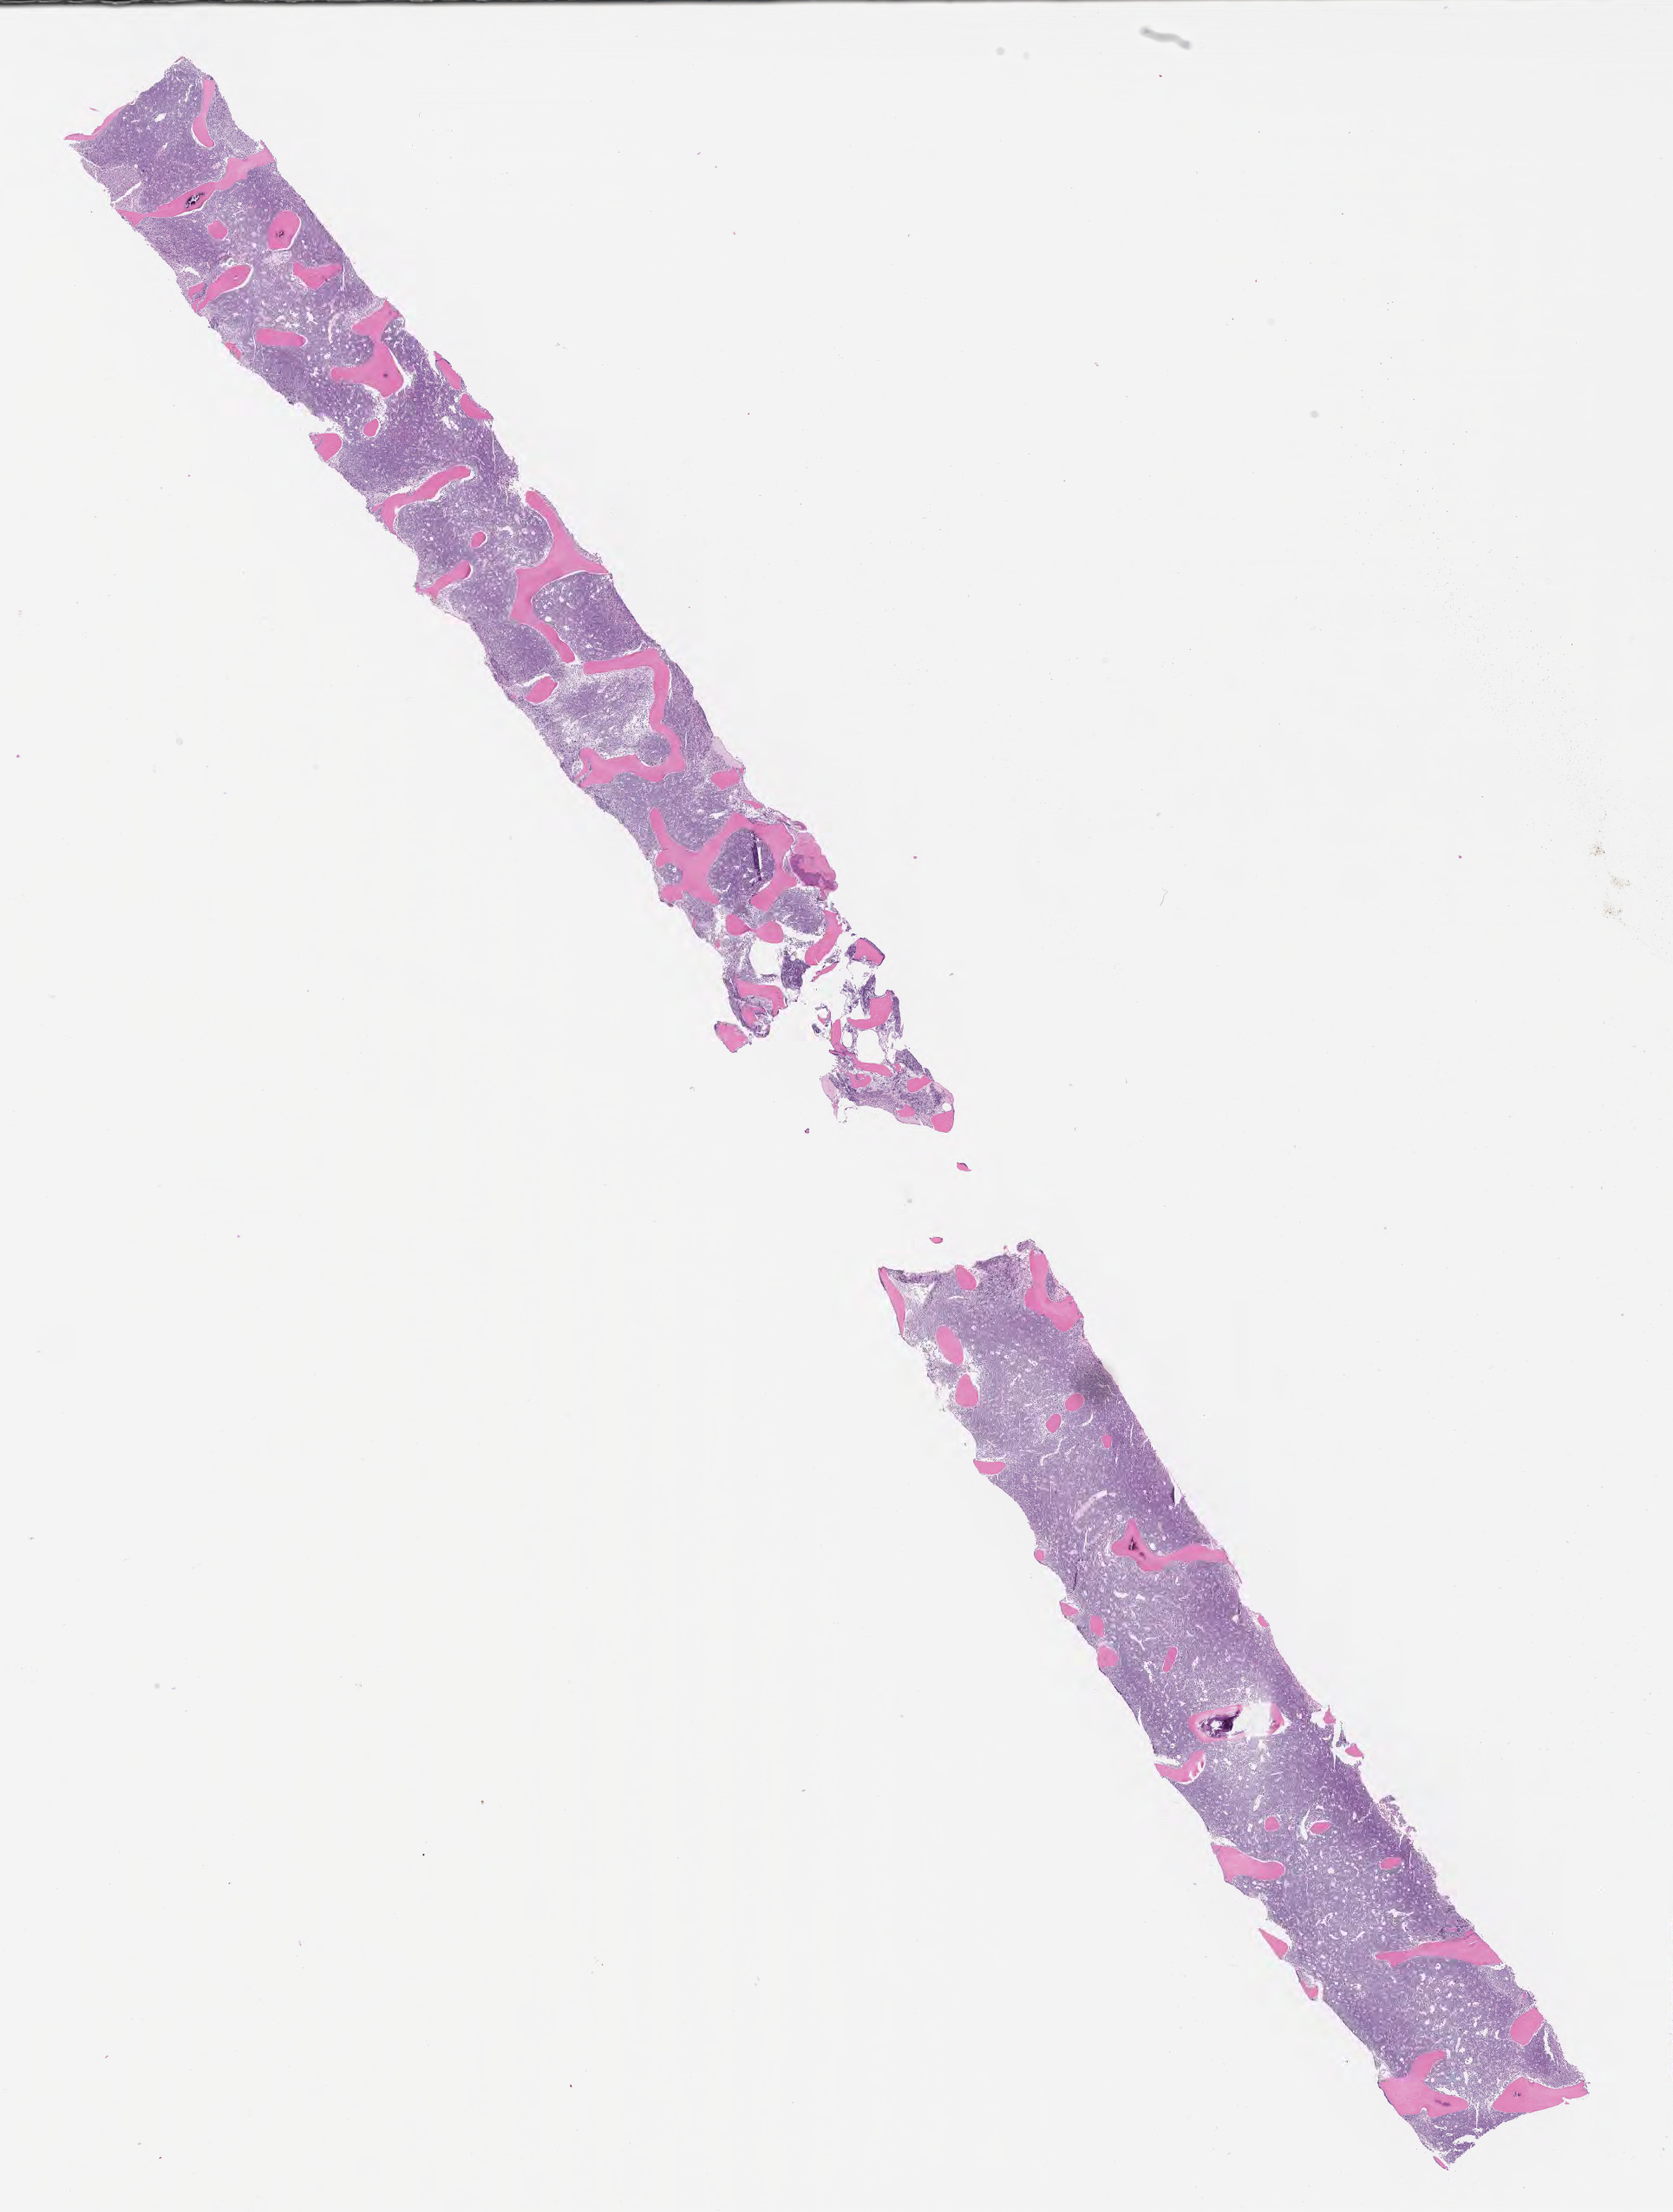
Whole-slide image, H&E stain, whole scanned area (about 15.6 x 20.6 mm) shown as a low-resolution overview. Tumor tissue. Patient: male, age at initial diagnosis 7 years.
• diagnosis: Burkitt lymphoma, NOS